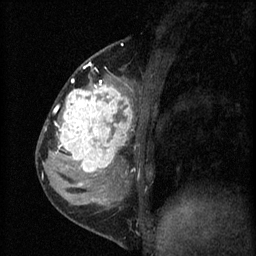
Breast MRI (dynamic contrast-enhanced), one sagittal slice. Position 22 of 60 along the scan axis. 3 images stored at this slice position (order not interpretable as contrast timing). 1.5 T. TE 4.2 ms, TR 8.2 ms. 256 × 256 image matrix, field of view 180 × 180 mm. Female patient, age 37 years.
Annotated regions visible in this slice (semi-automatically segmented with operator editing):
- analysis volume of interest (the breast-tissue region the enhancement analysis was run in; not a lesion): bounding box (x1, y1, x2, y2) in pixels: (53, 78, 140, 181)
- tumour enhancement mask (voxels above the 70 % enhancement threshold inside the analysis volume of interest): (56, 78, 133, 177)